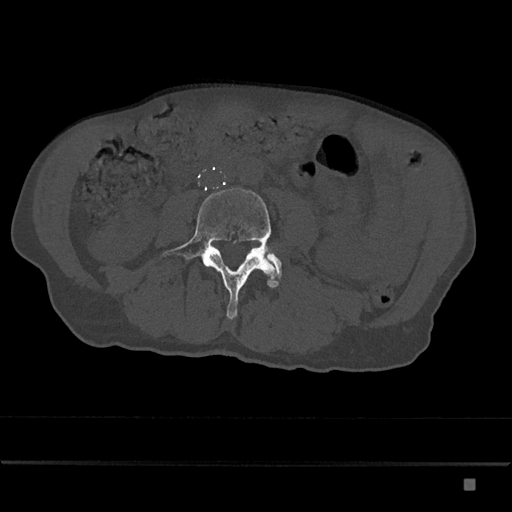
CT including the spine, one axial slice. Position 338 of 797 along the scan axis. Reconstruction kernel Br40s/3. Bone window (W 1800 / L 400 HU). 512 × 512 image matrix, field of view 390 × 390 mm. Male patient, age 72 years. Case-level facts recorded for this patient, not image findings: primary cancer: prostate.
Structures marked on this image (semi-automatically segmented with operator editing):
- L4 vertebra: box from (x=162, y=188) to (x=281, y=319) px
- L5 vertebra: (x=268, y=254)–(x=281, y=271)